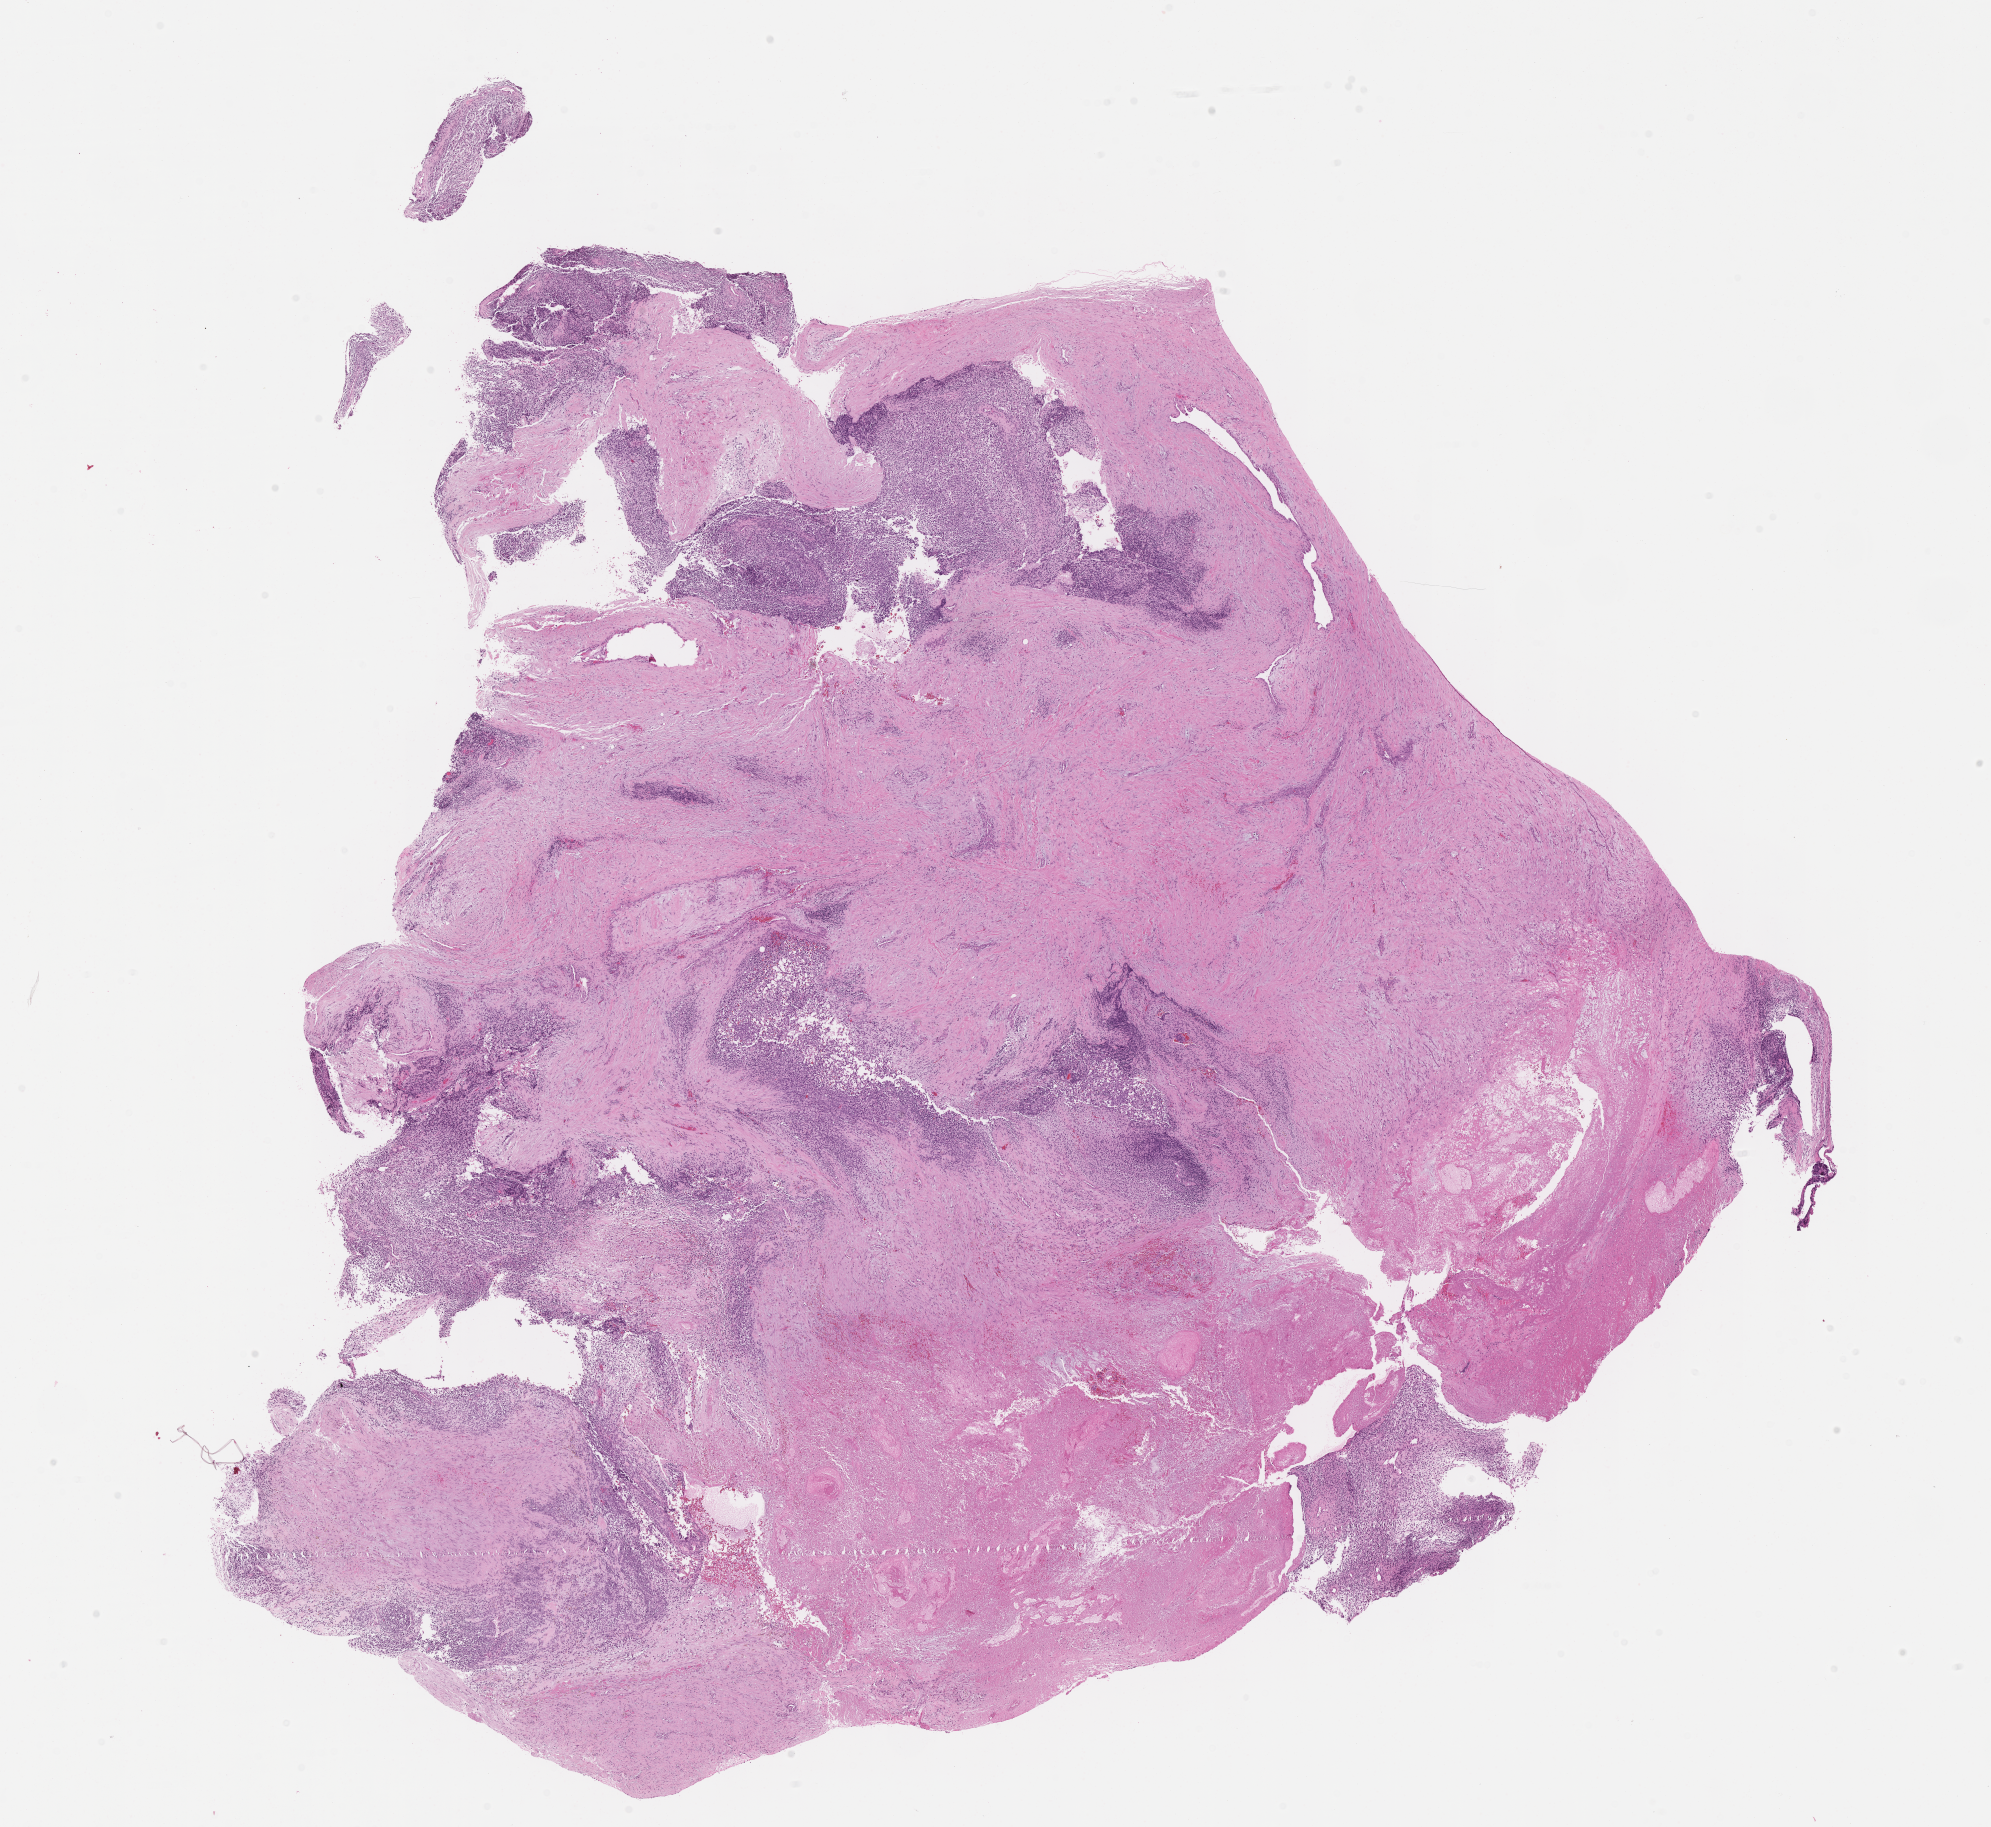
Digitized H&E-stained section of tumor tissue, whole scanned area (about 16.1 x 14.8 mm) shown as a low-resolution overview. Formalin-fixed, paraffin-embedded (FFPE) tissue. Sample anatomic site: pelvis. Female patient, age at diagnosis 4.3 years.
Diagnosis: rhabdomyosarcoma; histological classification: embryonal rhabdomyosarcoma. Metastatic status at presentation (as recorded): metastatic (confirmed). Stage (as recorded): 4.